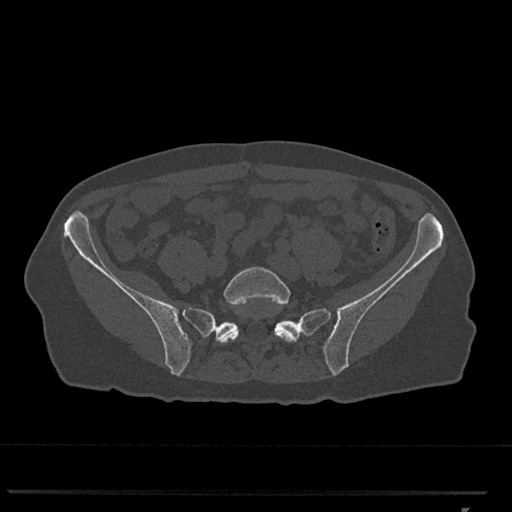
CT including the spine, one axial slice; slice 126 of 793 in the series (ordered by position); 120 kVp; bone window (W 1800 / L 400 HU); 512 × 512 image matrix, field of view 380 × 380 mm. Female patient, age 62 years. Case-level facts recorded for this patient, not image findings: primary cancer: renal.
Annotated regions visible in this slice (semi-automatically segmented with operator editing):
- L5 vertebra: bounding box <218,267,298,343> (left, top, right, bottom; pixels)